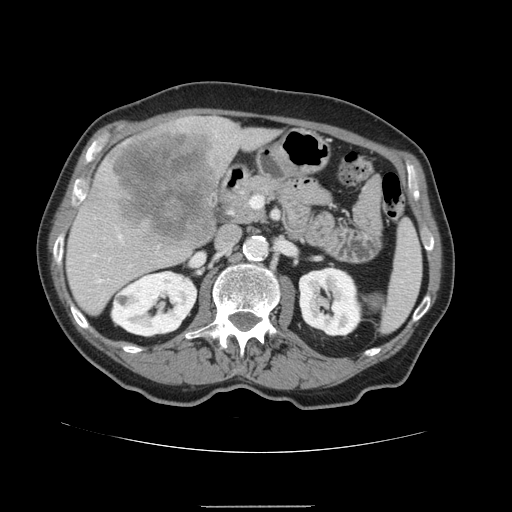
Contrast-enhanced abdominal CT, one axial slice. Position 73 of 168 along the scan axis. Soft-tissue window (W 400 / L 40 HU). 512 × 512 image matrix, field of view 386 × 386 mm. Male patient, age 74 years. From the clinical record (not read from this slice): diagnosis: colorectal cancer liver metastases, imaged before liver resection.
Outlined on this slice (outlined manually by an expert reader):
- liver: bounding box (x1, y1, x2, y2) in pixels: (66, 116, 281, 316)
- planned liver remnant (the part of the liver to remain after resection): (66, 126, 280, 316)
- liver metastasis: (112, 125, 220, 247)